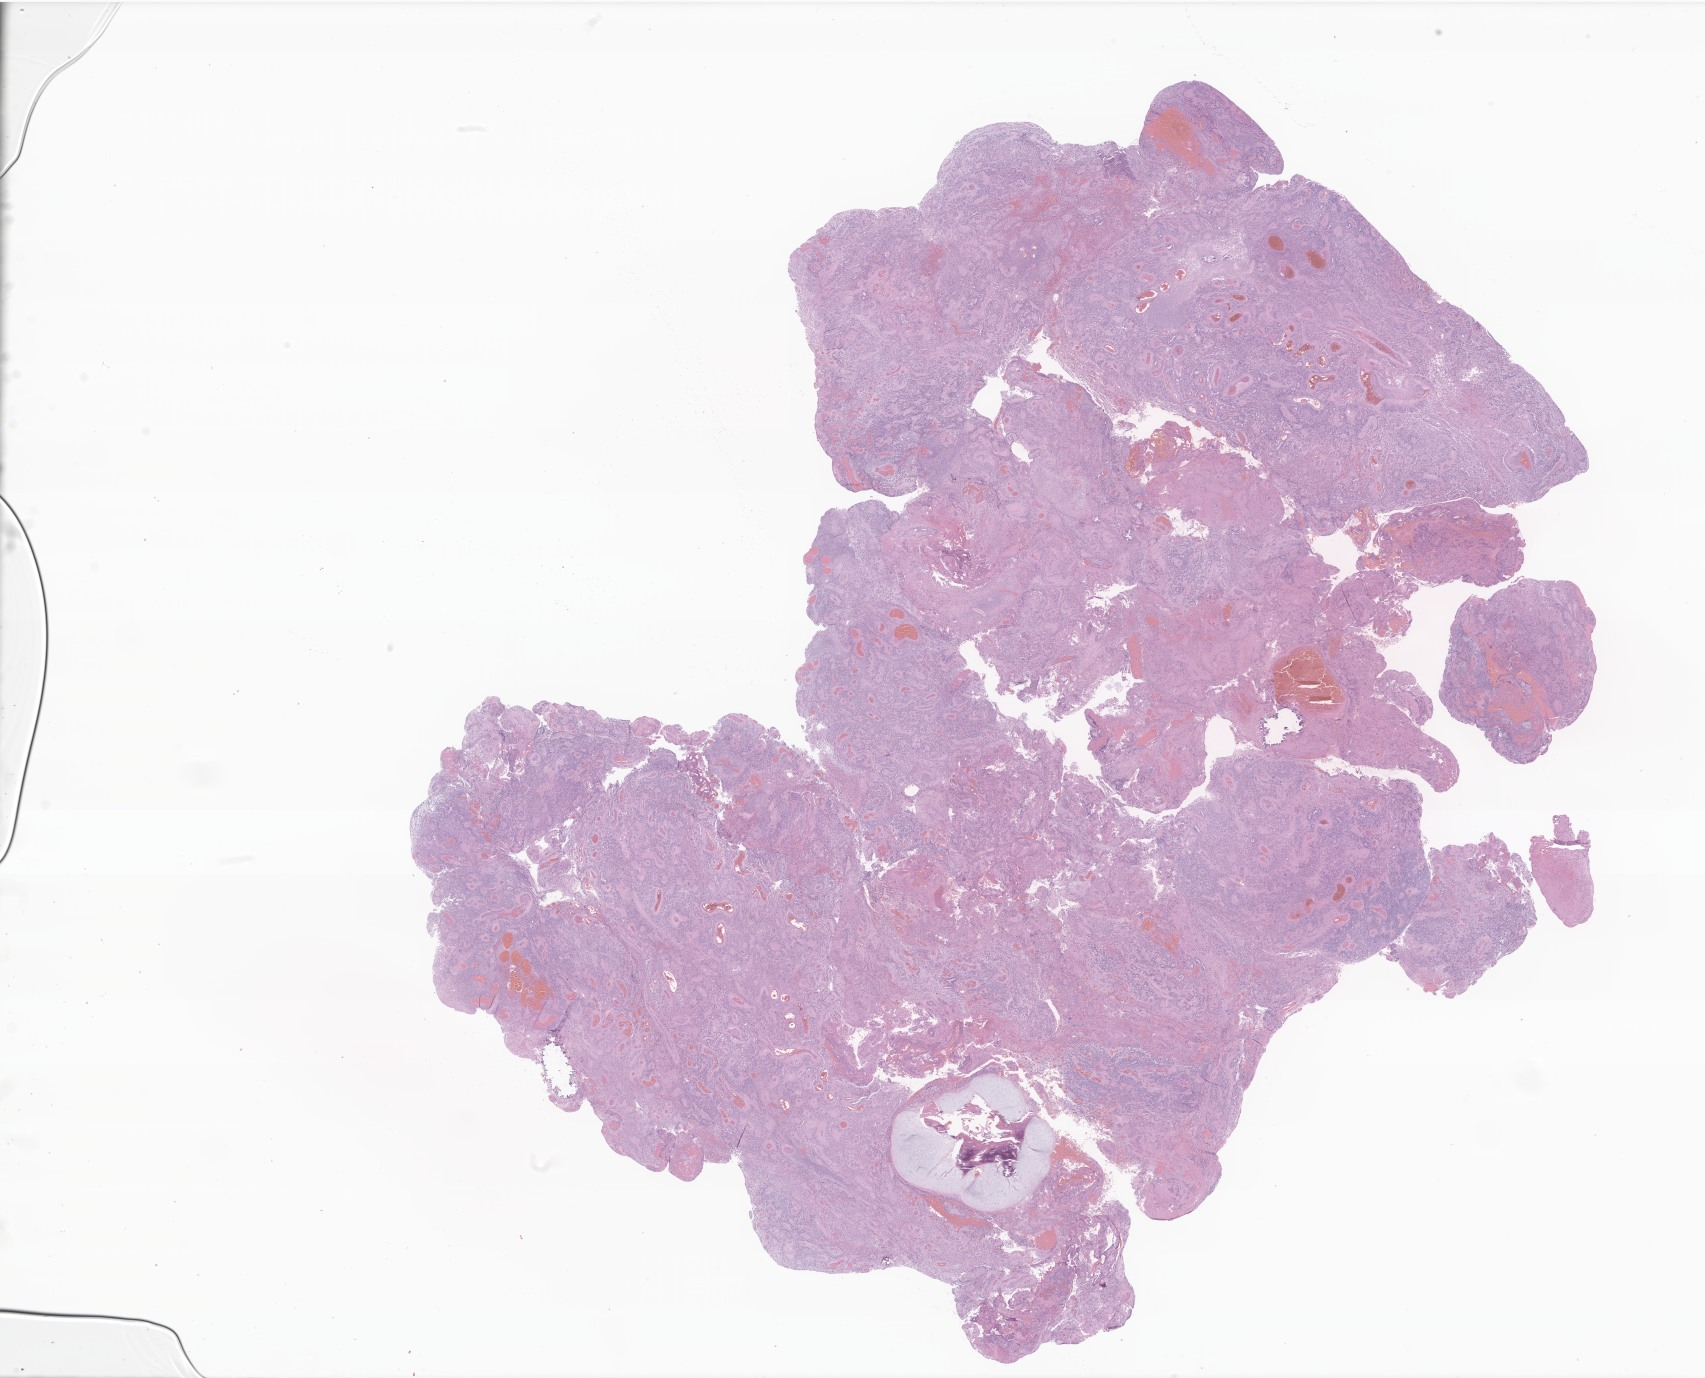
Whole-slide image, haematoxylin and eosin stain of tumor tissue from the cerebral ventricle, low-resolution overview of the scanned area, about 28.8 x 23.2 mm. Formalin-fixed paraffin-embedded section. Patient male; age 958 days (about 2.6 years).
Recorded diagnosis: Neoplasm, malignant.